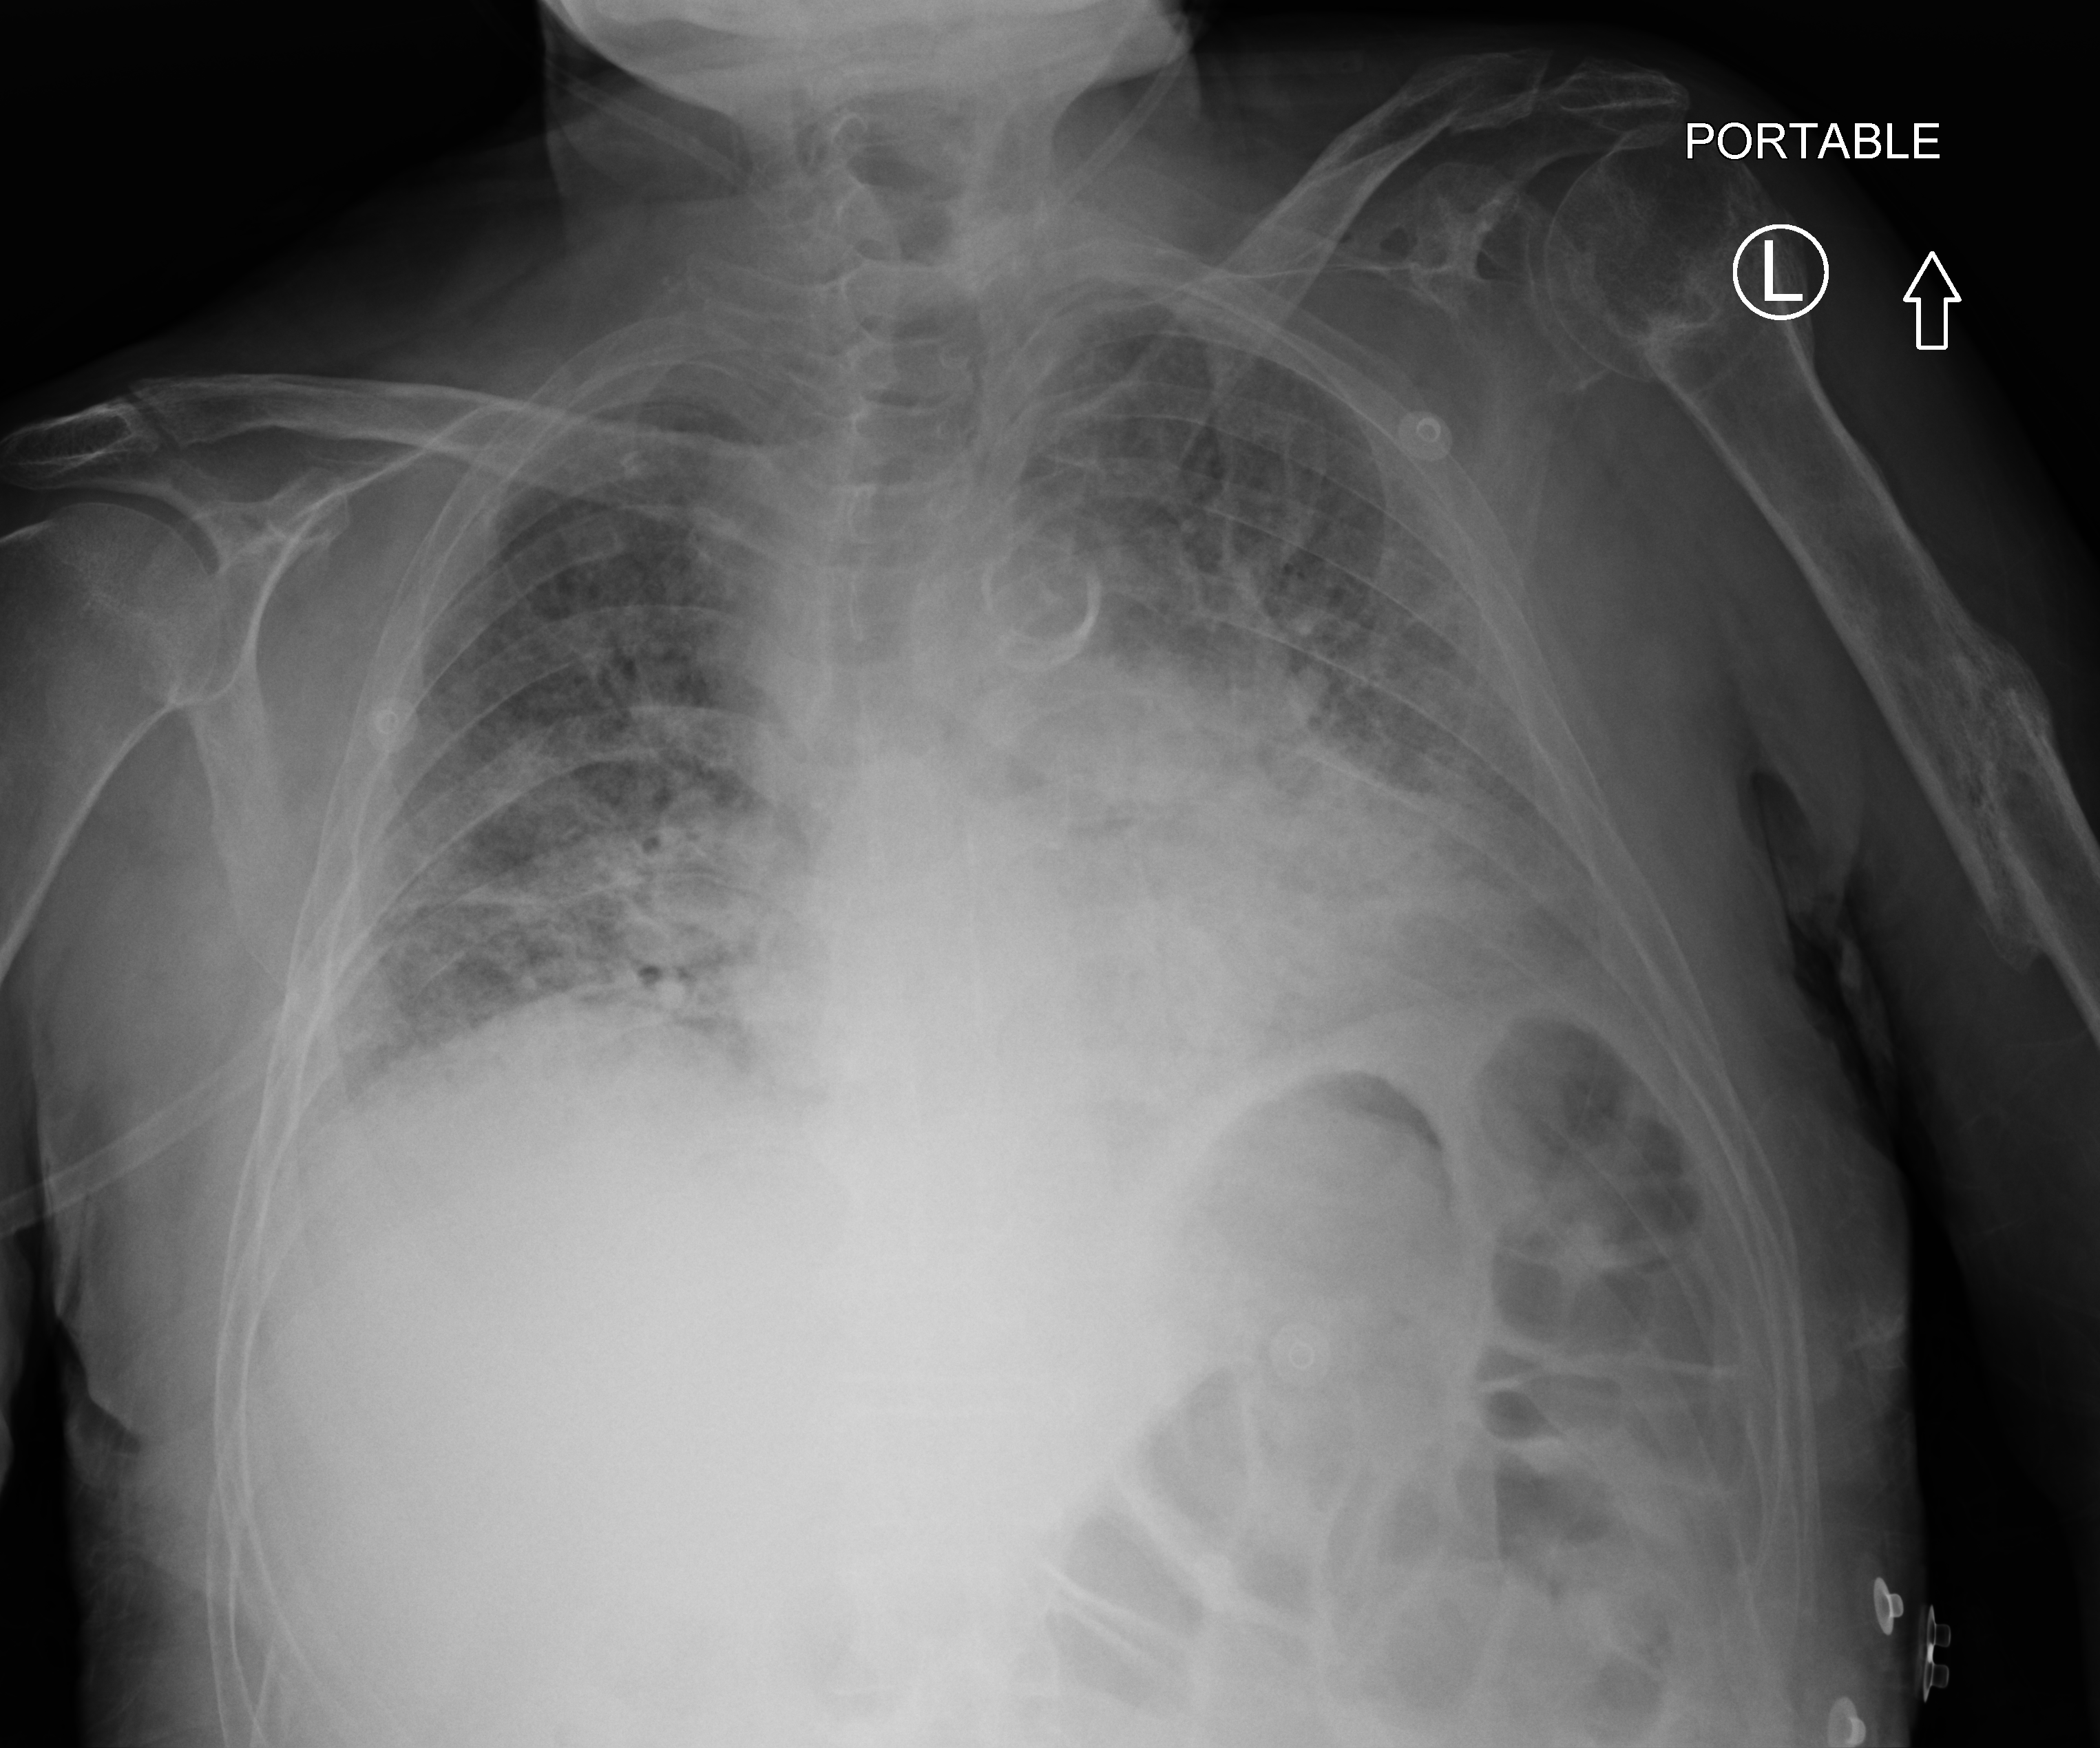
Portable chest radiograph, anteroposterior (AP) projection. Patient hospitalised with COVID-19; male, aged 60–74 years.
Admission-level facts for this patient (not findings on this image; timing relative to this image not recorded): admitted to intensive care during this hospital stay: no; mechanically ventilated during this hospital stay: no.